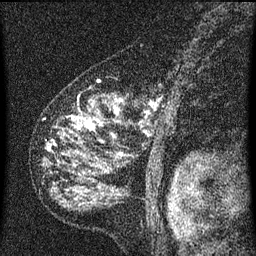
Breast MRI (dynamic contrast-enhanced), one sagittal slice; dynamic contrast-enhanced series, image 2 of 3 at this slice position (ordered by acquisition); 1.5 T; TE 4.2 ms, TR 8 ms; 2 mm slice thickness; 256 × 256 image matrix. Patient: female, 55 years.
Structures marked on this image (semi-automatic segmentation, software-assisted and operator-edited):
- analysis volume of interest (the breast-tissue region the enhancement analysis was run in; not a lesion): bounding box <45,90,184,155> (left, top, right, bottom; pixels)
- tumour enhancement mask (voxels above the 70 % enhancement threshold inside the analysis volume of interest): <86,110,118,131>